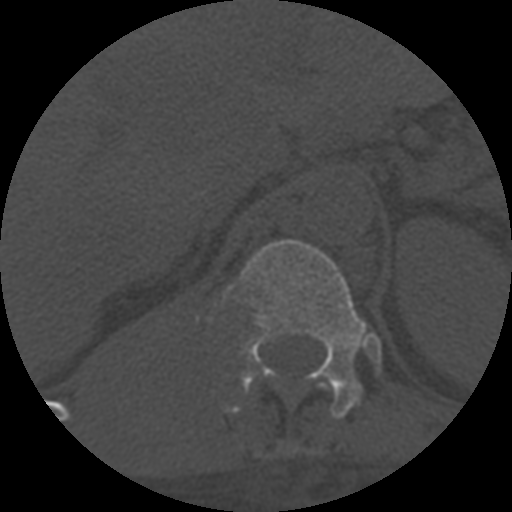
CT including the spine, one axial slice. Slice 319 of 708 in the series (ordered by position). 120 kVp. One of 3 acquisitions stored at this slice position. Bone window (W 1800 / L 400 HU). 512 × 512 image matrix, field of view 160 × 160 mm. Patient age 55 years. From the clinical record (not read from this slice): primary cancer: colon; vertebrae with lytic lesions (as recorded): T12, L1, L5.
Outlined on this slice (semi-automatic segmentation, software-assisted and operator-edited):
- T11 vertebra: bounding box <246,383,329,390> (left, top, right, bottom; pixels)
- T12 vertebra: <222,240,367,419>